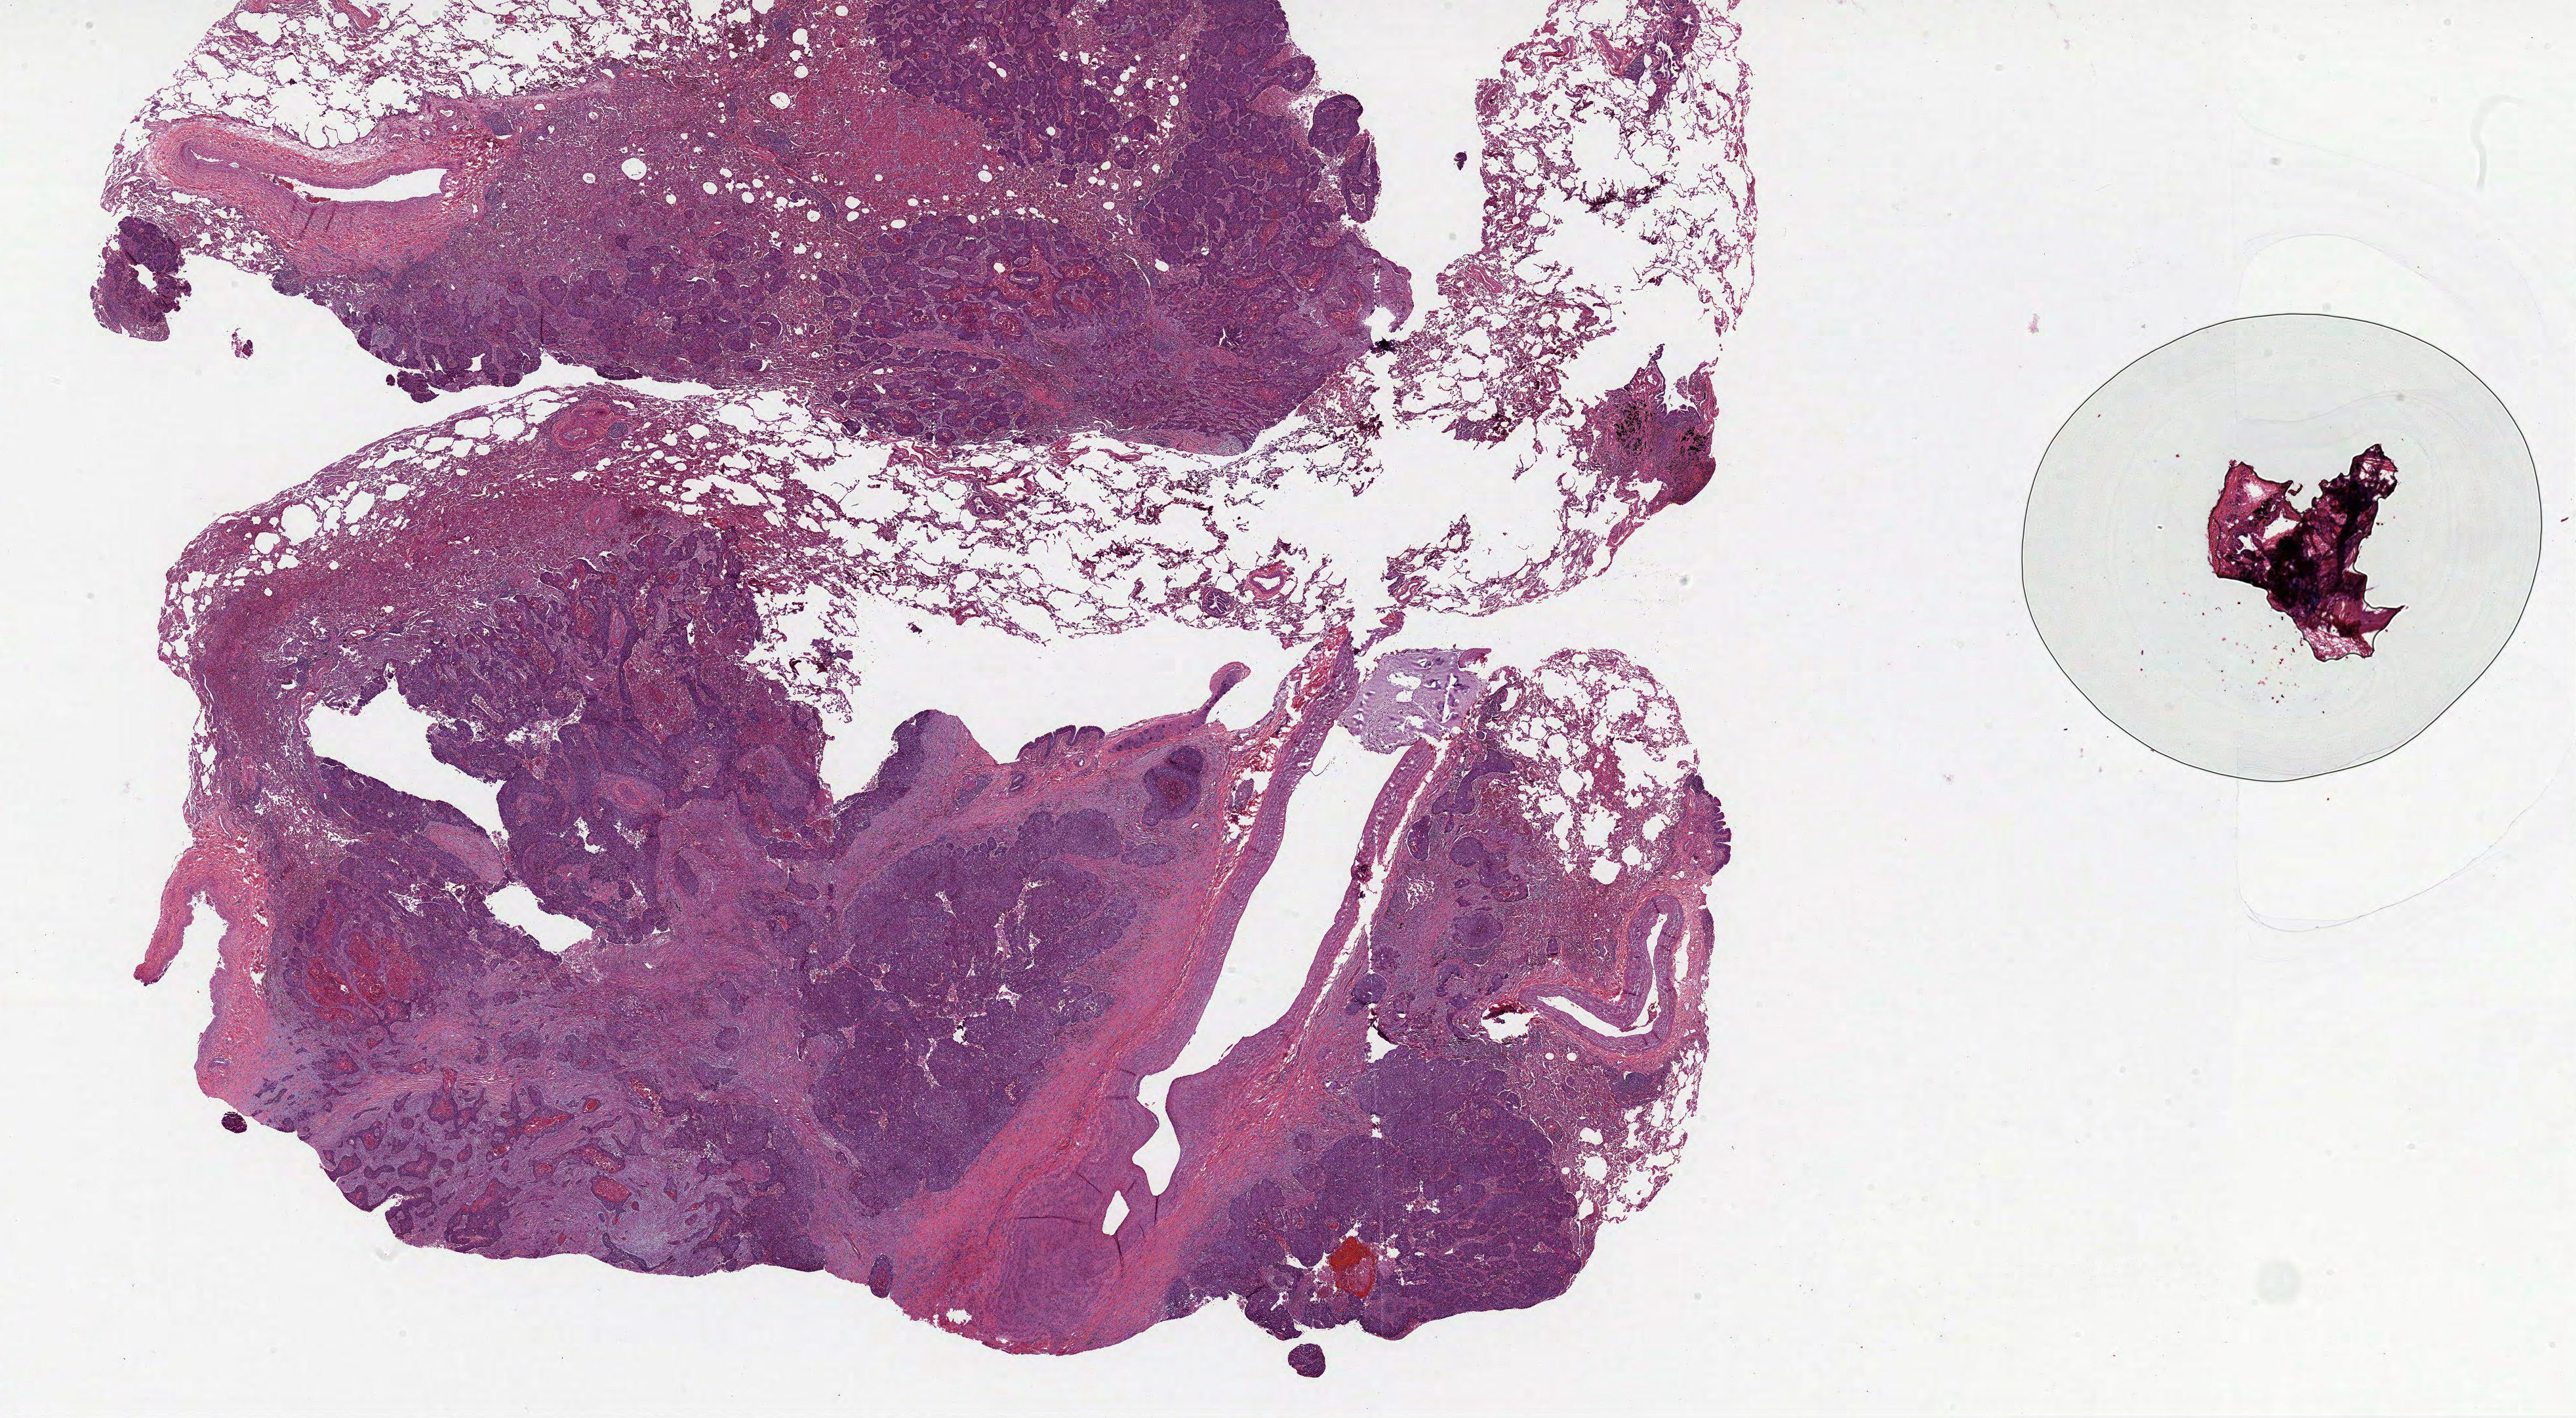
Whole-slide histology image, H&E — a low-resolution overview of the entire scanned area, about 31.7 x 17.4 mm, formalin-fixed paraffin-embedded (FFPE) diagnostic section, primary tumour sample from the lung. Patient: male, age at initial diagnosis 65 years.
Diagnosis: Squamous cell carcinoma, NOS (lower lobe, lung). TNM: T1b N1 M0. AJCC pathologic stage: IIA (6th edition). Laterality: left.